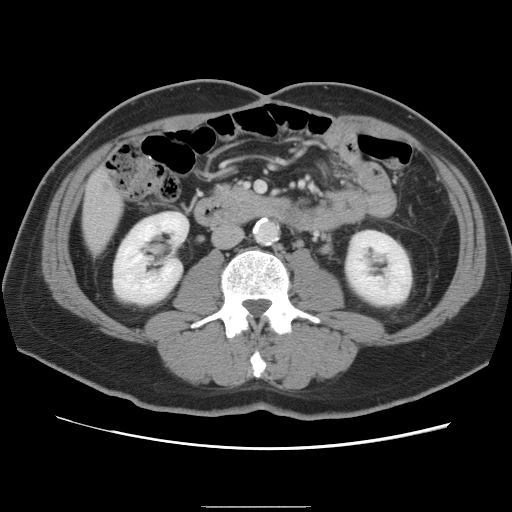
Contrast-enhanced abdominal CT, one axial slice. Position 20 of 87 along the scan axis. Intravenous contrast given. Soft-tissue window (W 400 / L 40 HU). 5 mm slice thickness. 512 × 512 image matrix. Male patient, age 63 years. From the clinical record (not read from this slice): diagnosis: colorectal cancer liver metastases, imaged before liver resection; multiple liver metastases: no; largest metastasis: 9 cm; chemotherapy before resection: no.
Structures marked on this image (manually delineated by an expert):
- liver: bounding box (x1, y1, x2, y2) in pixels: (84, 170, 124, 251)
- planned liver remnant (the part of the liver to remain after resection): (84, 170, 124, 252)
- liver metastasis: (105, 181, 112, 189)